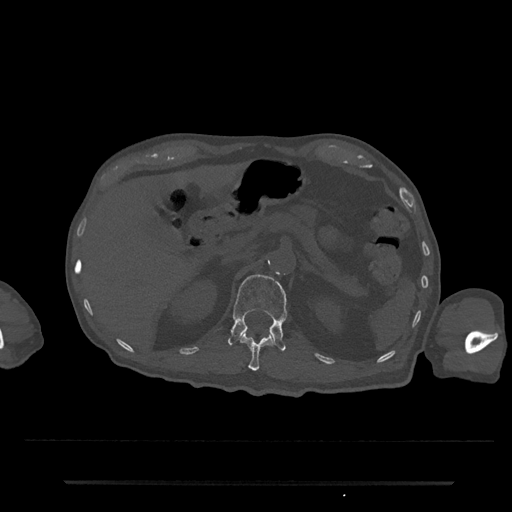
CT including the spine, one axial slice. Position 156 of 797 along the scan axis. Reconstruction kernel Br40s/3. 120 kVp. Bone window (W 1800 / L 400 HU). 0.5 mm slice thickness. 512 × 512 image matrix, field of view 427 × 427 mm. Patient: male, 74 years. Case-level facts recorded for this patient, not image findings: primary cancer: prostate.
Structures marked on this image (semi-automatic segmentation, software-assisted and operator-edited):
- L1 vertebra: bounding box <228,274,288,351> (left, top, right, bottom; pixels)
- T12 vertebra: <240,333,273,371>